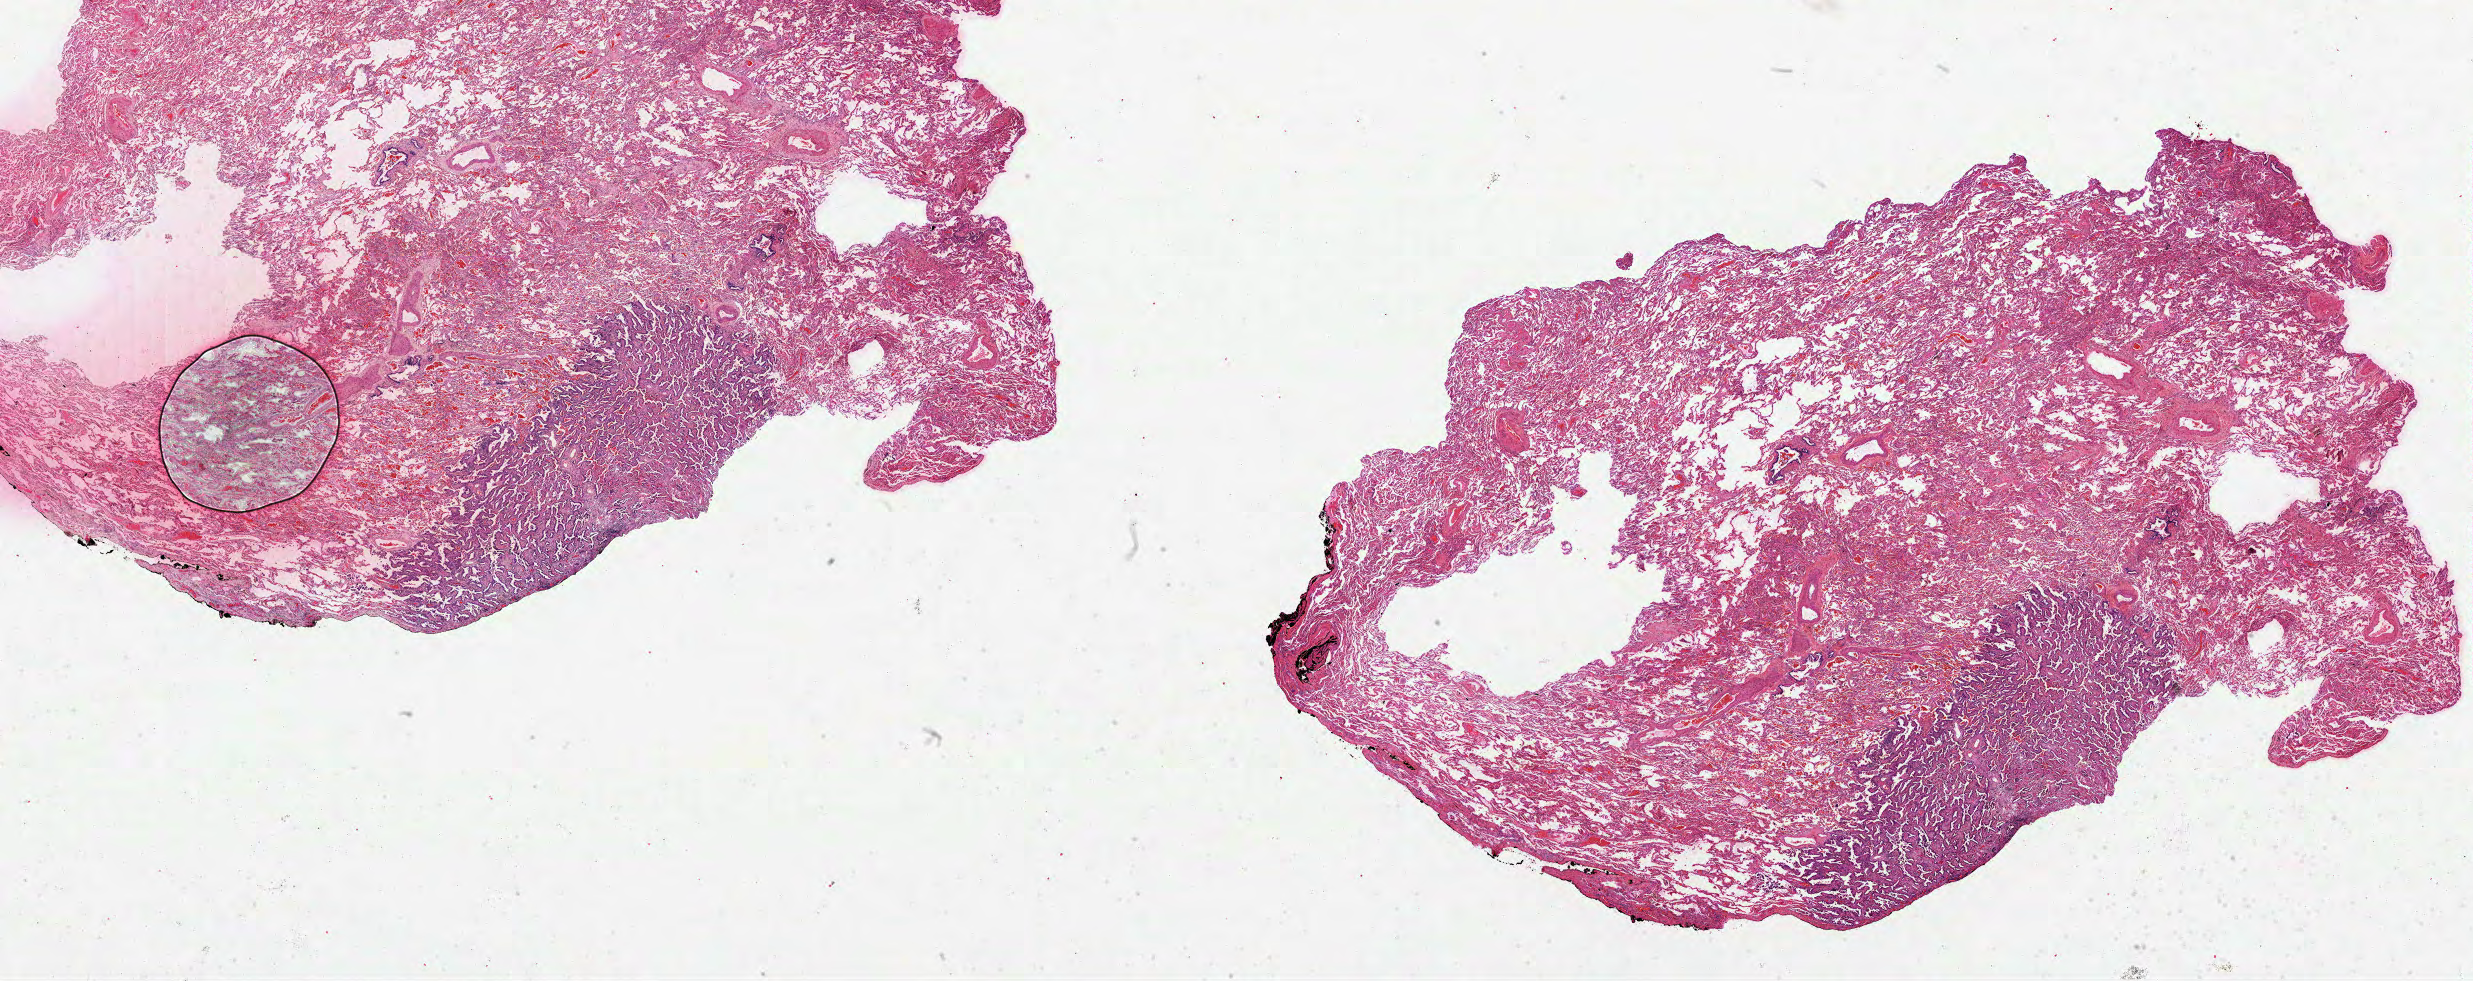
H&E-stained whole-slide image, shown as a low-resolution overview of the whole scanned area (about 39.9 x 15.8 mm), formalin-fixed paraffin-embedded (FFPE) diagnostic section, lung, primary tumour sample. Female patient; age at initial diagnosis 67 years.
• laterality: right
• AJCC pathologic stage: IB
• histologic diagnosis: Adenocarcinoma, NOS (upper lobe, lung)